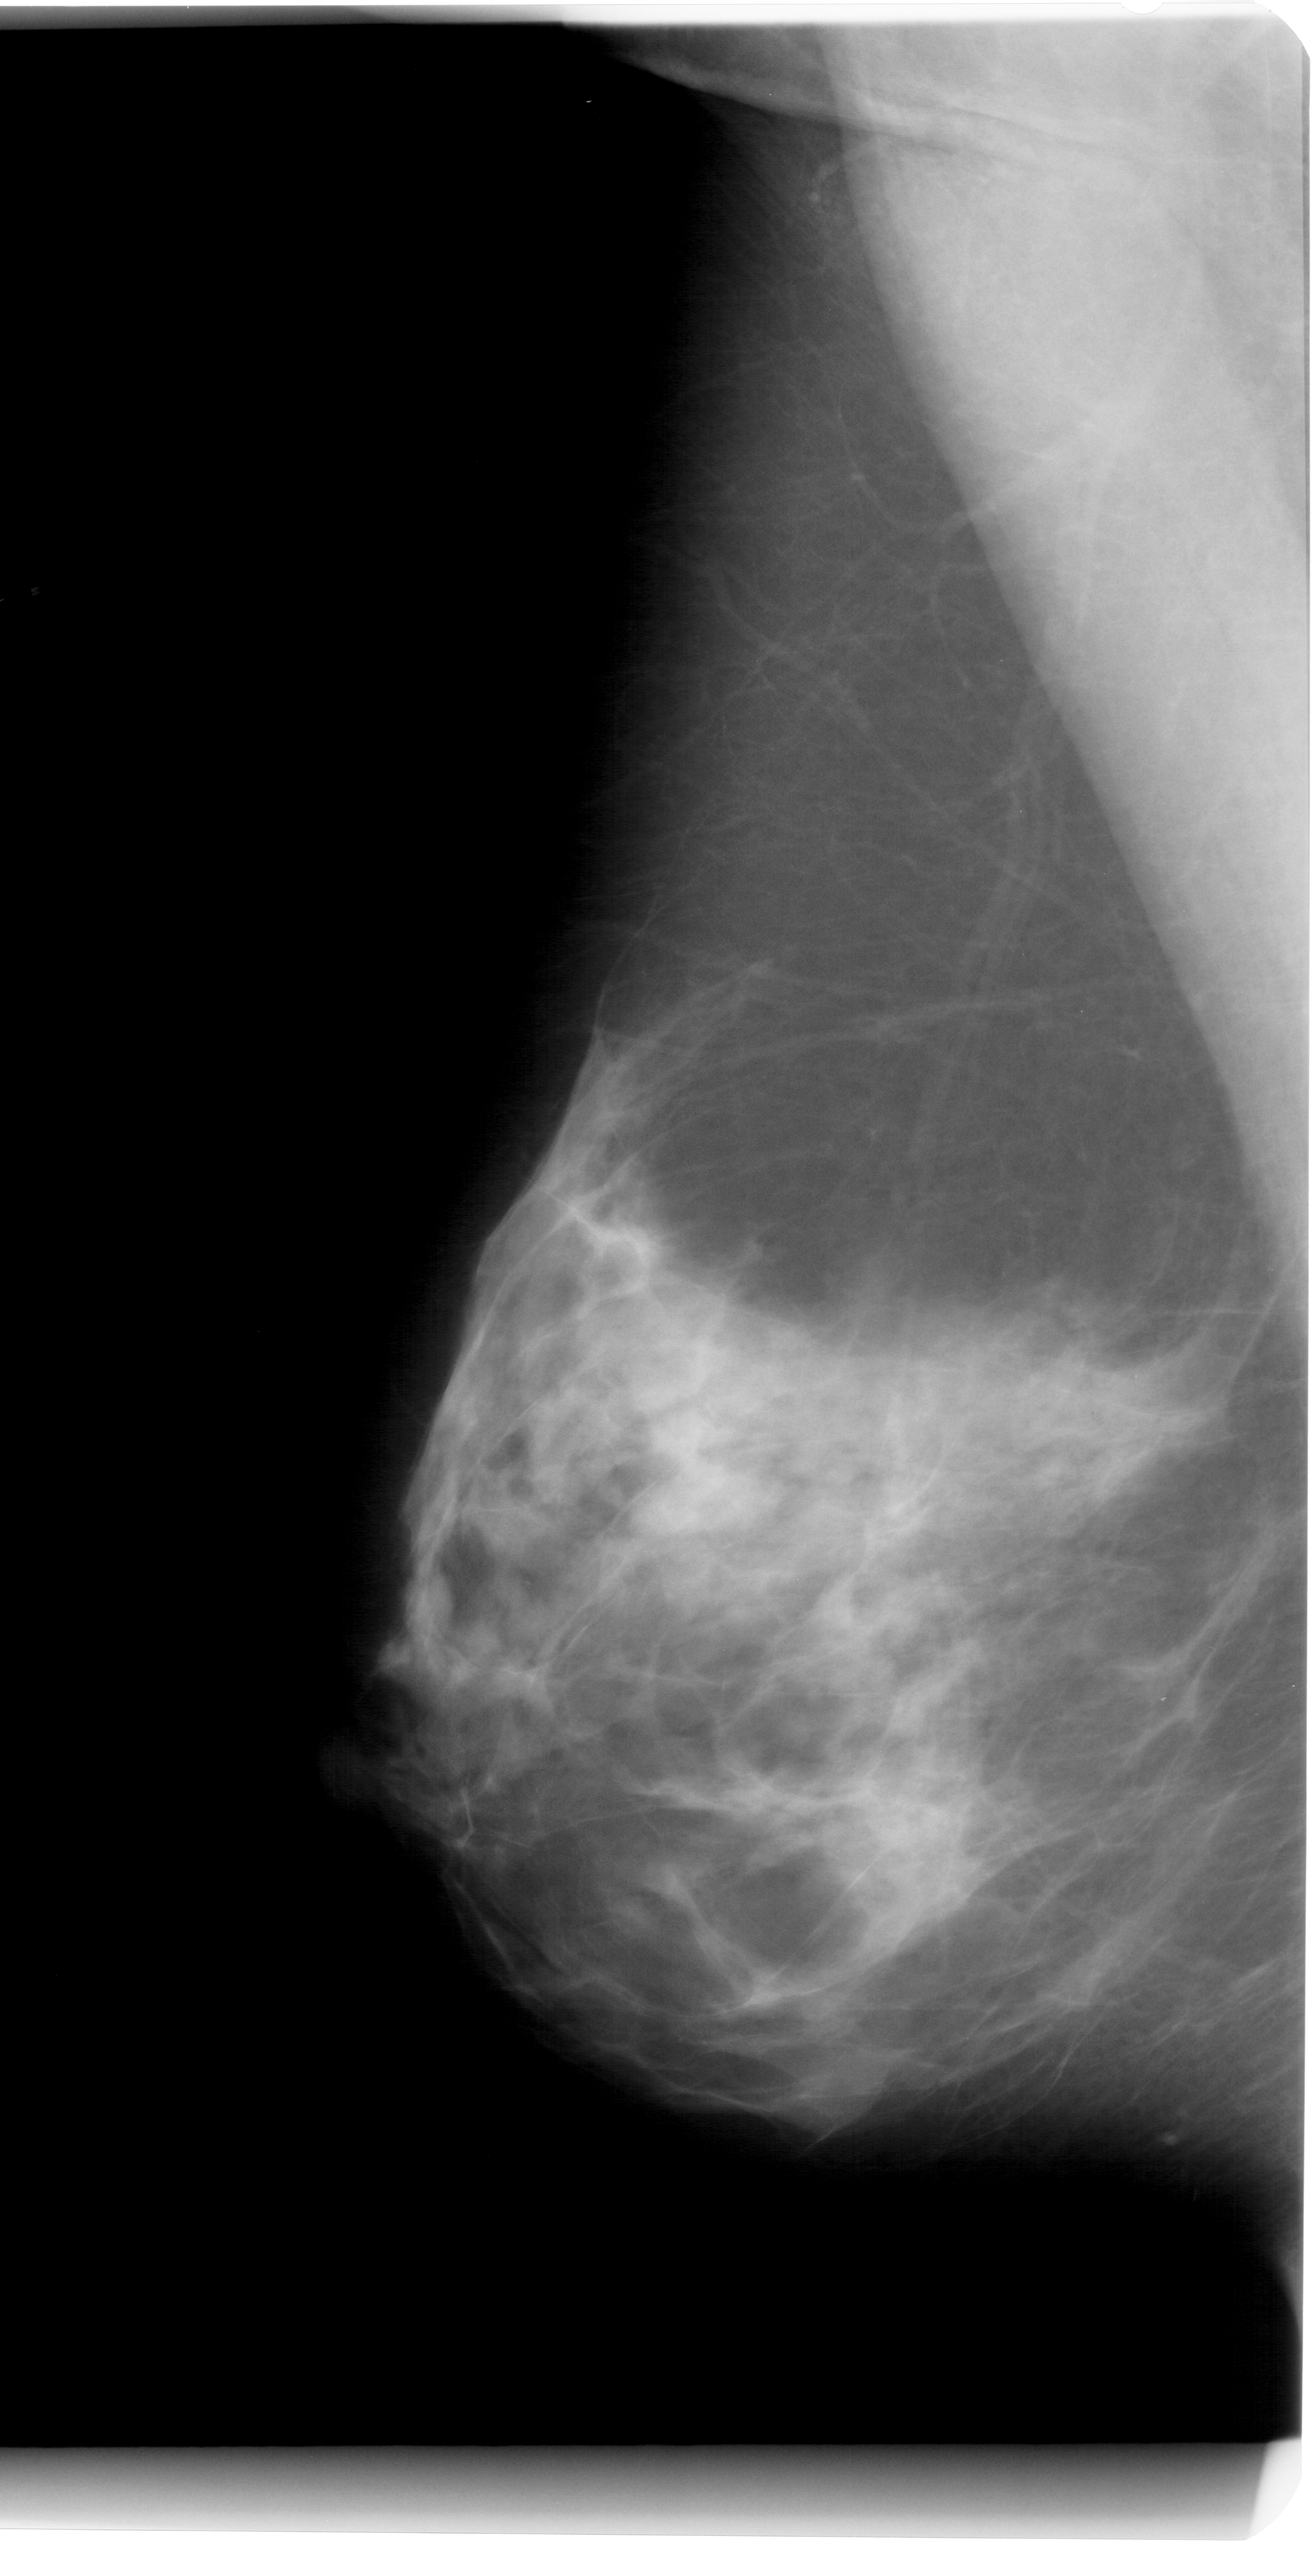
Digitized screen-film mammogram; left breast; MLO view; BI-RADS breast density category 4 (scale 1–4).
- Radiologist-marked abnormalities on this image: mass, shape irregular, margins ill defined; BI-RADS assessment category 4; subtlety rating 3 on a 1 (subtle) to 5 (obvious) scale; pathology (as recorded): benign.